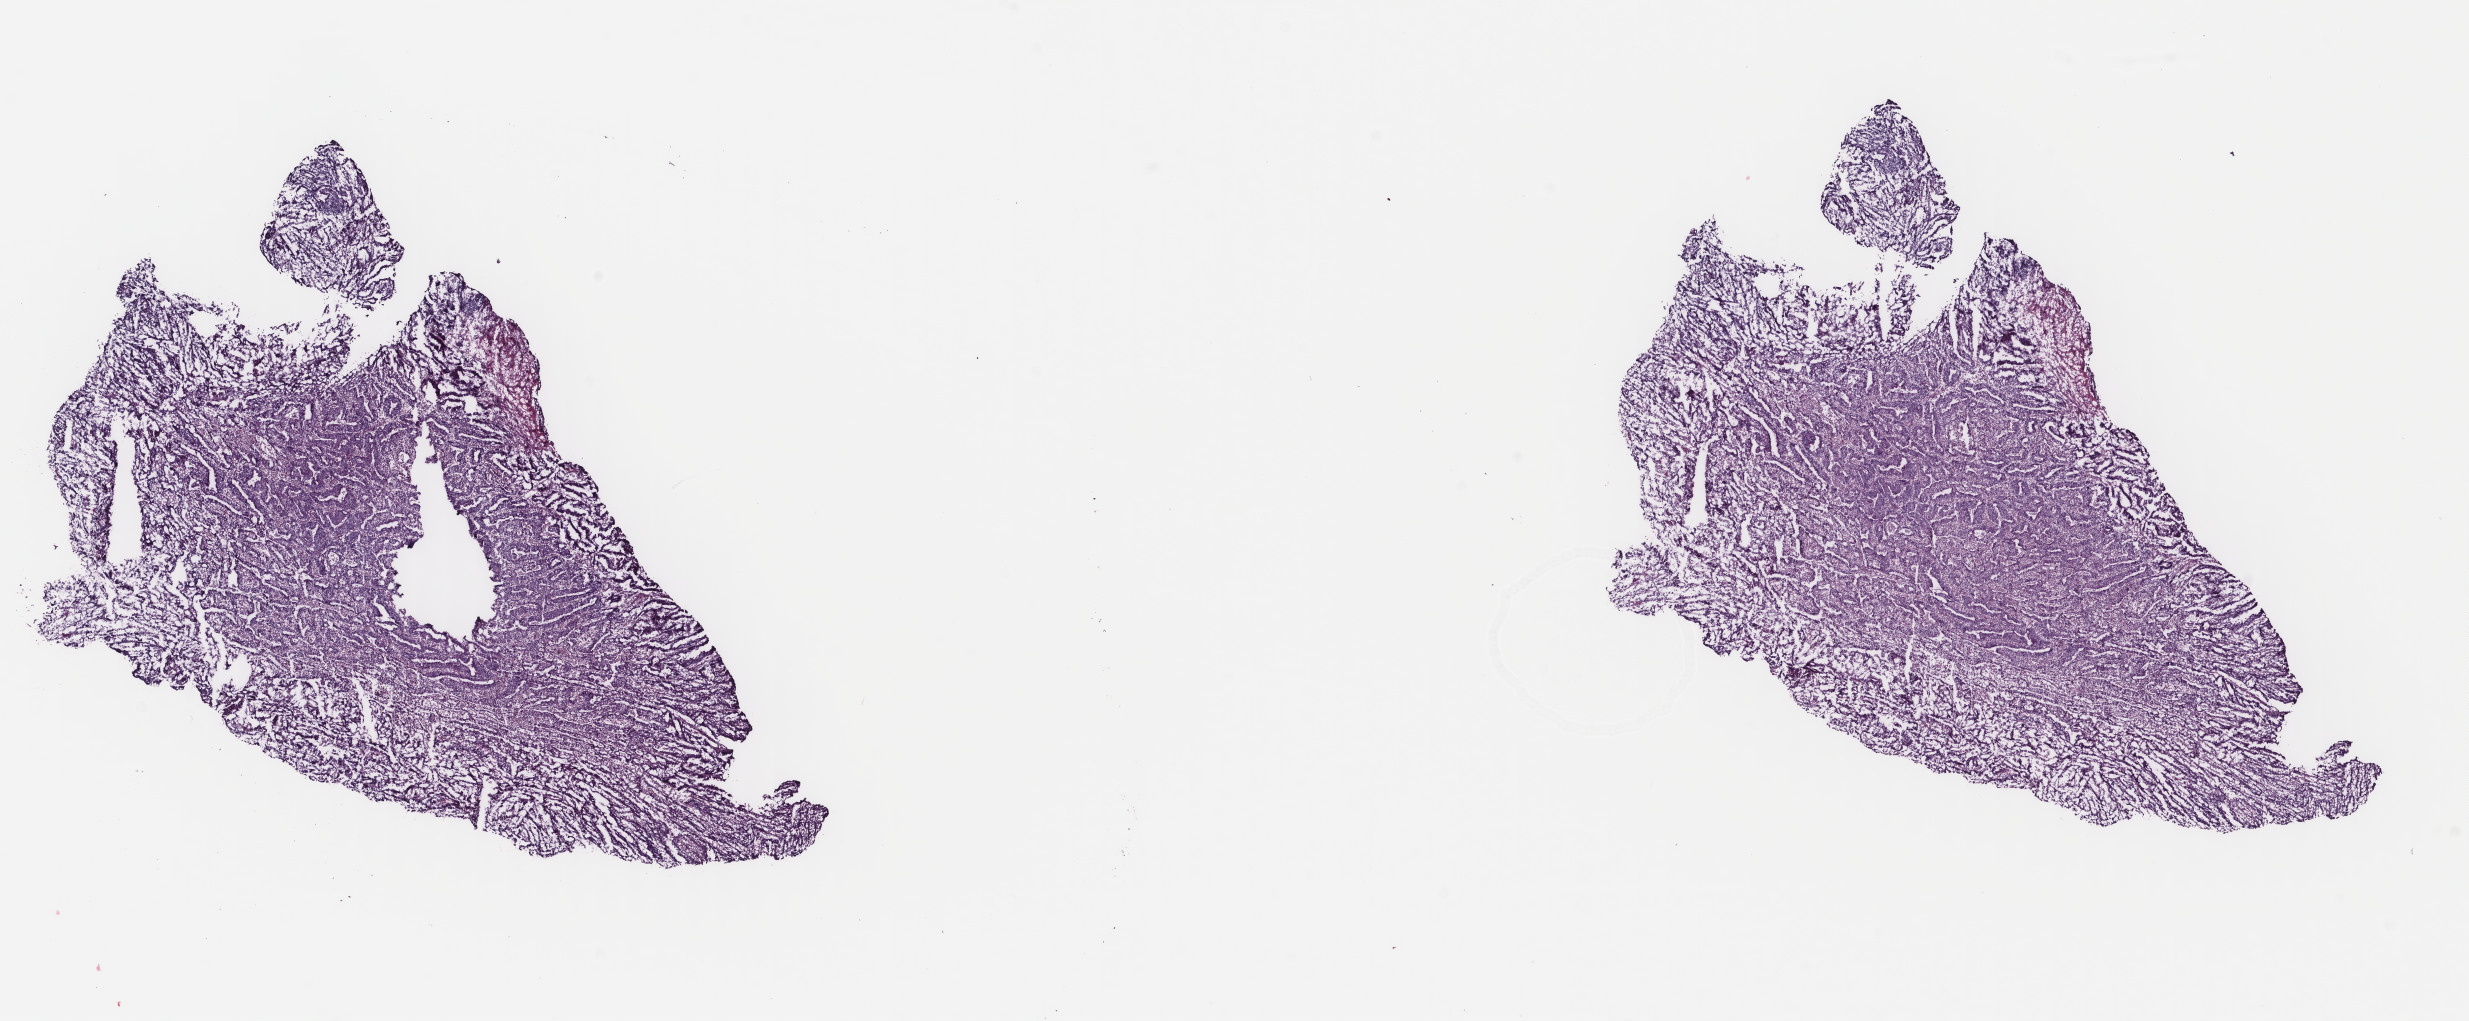
Digitized Hematoxylin and eosin (H&E) stained tissue section (whole slide) — low-resolution overview of the scanned area, about 19.6 x 8.1 mm (acquisition: 40x scan), frozen section from the top of the tissue portion, uterus, primary tumour sample. Patient: female, age at initial diagnosis 55 years. Histologic grade: G3 (poorly differentiated). Slide review estimates, as recorded: tumour cells 85%, tumour nuclei 85%, normal cells 0%, stromal cells 15%, necrosis 0%. Inflammatory infiltration, as recorded: lymphocyte infiltration 5%, monocyte infiltration 5%, neutrophil infiltration 25%.
FIGO stage: IB. Histologic diagnosis: Endometrioid adenocarcinoma, NOS.